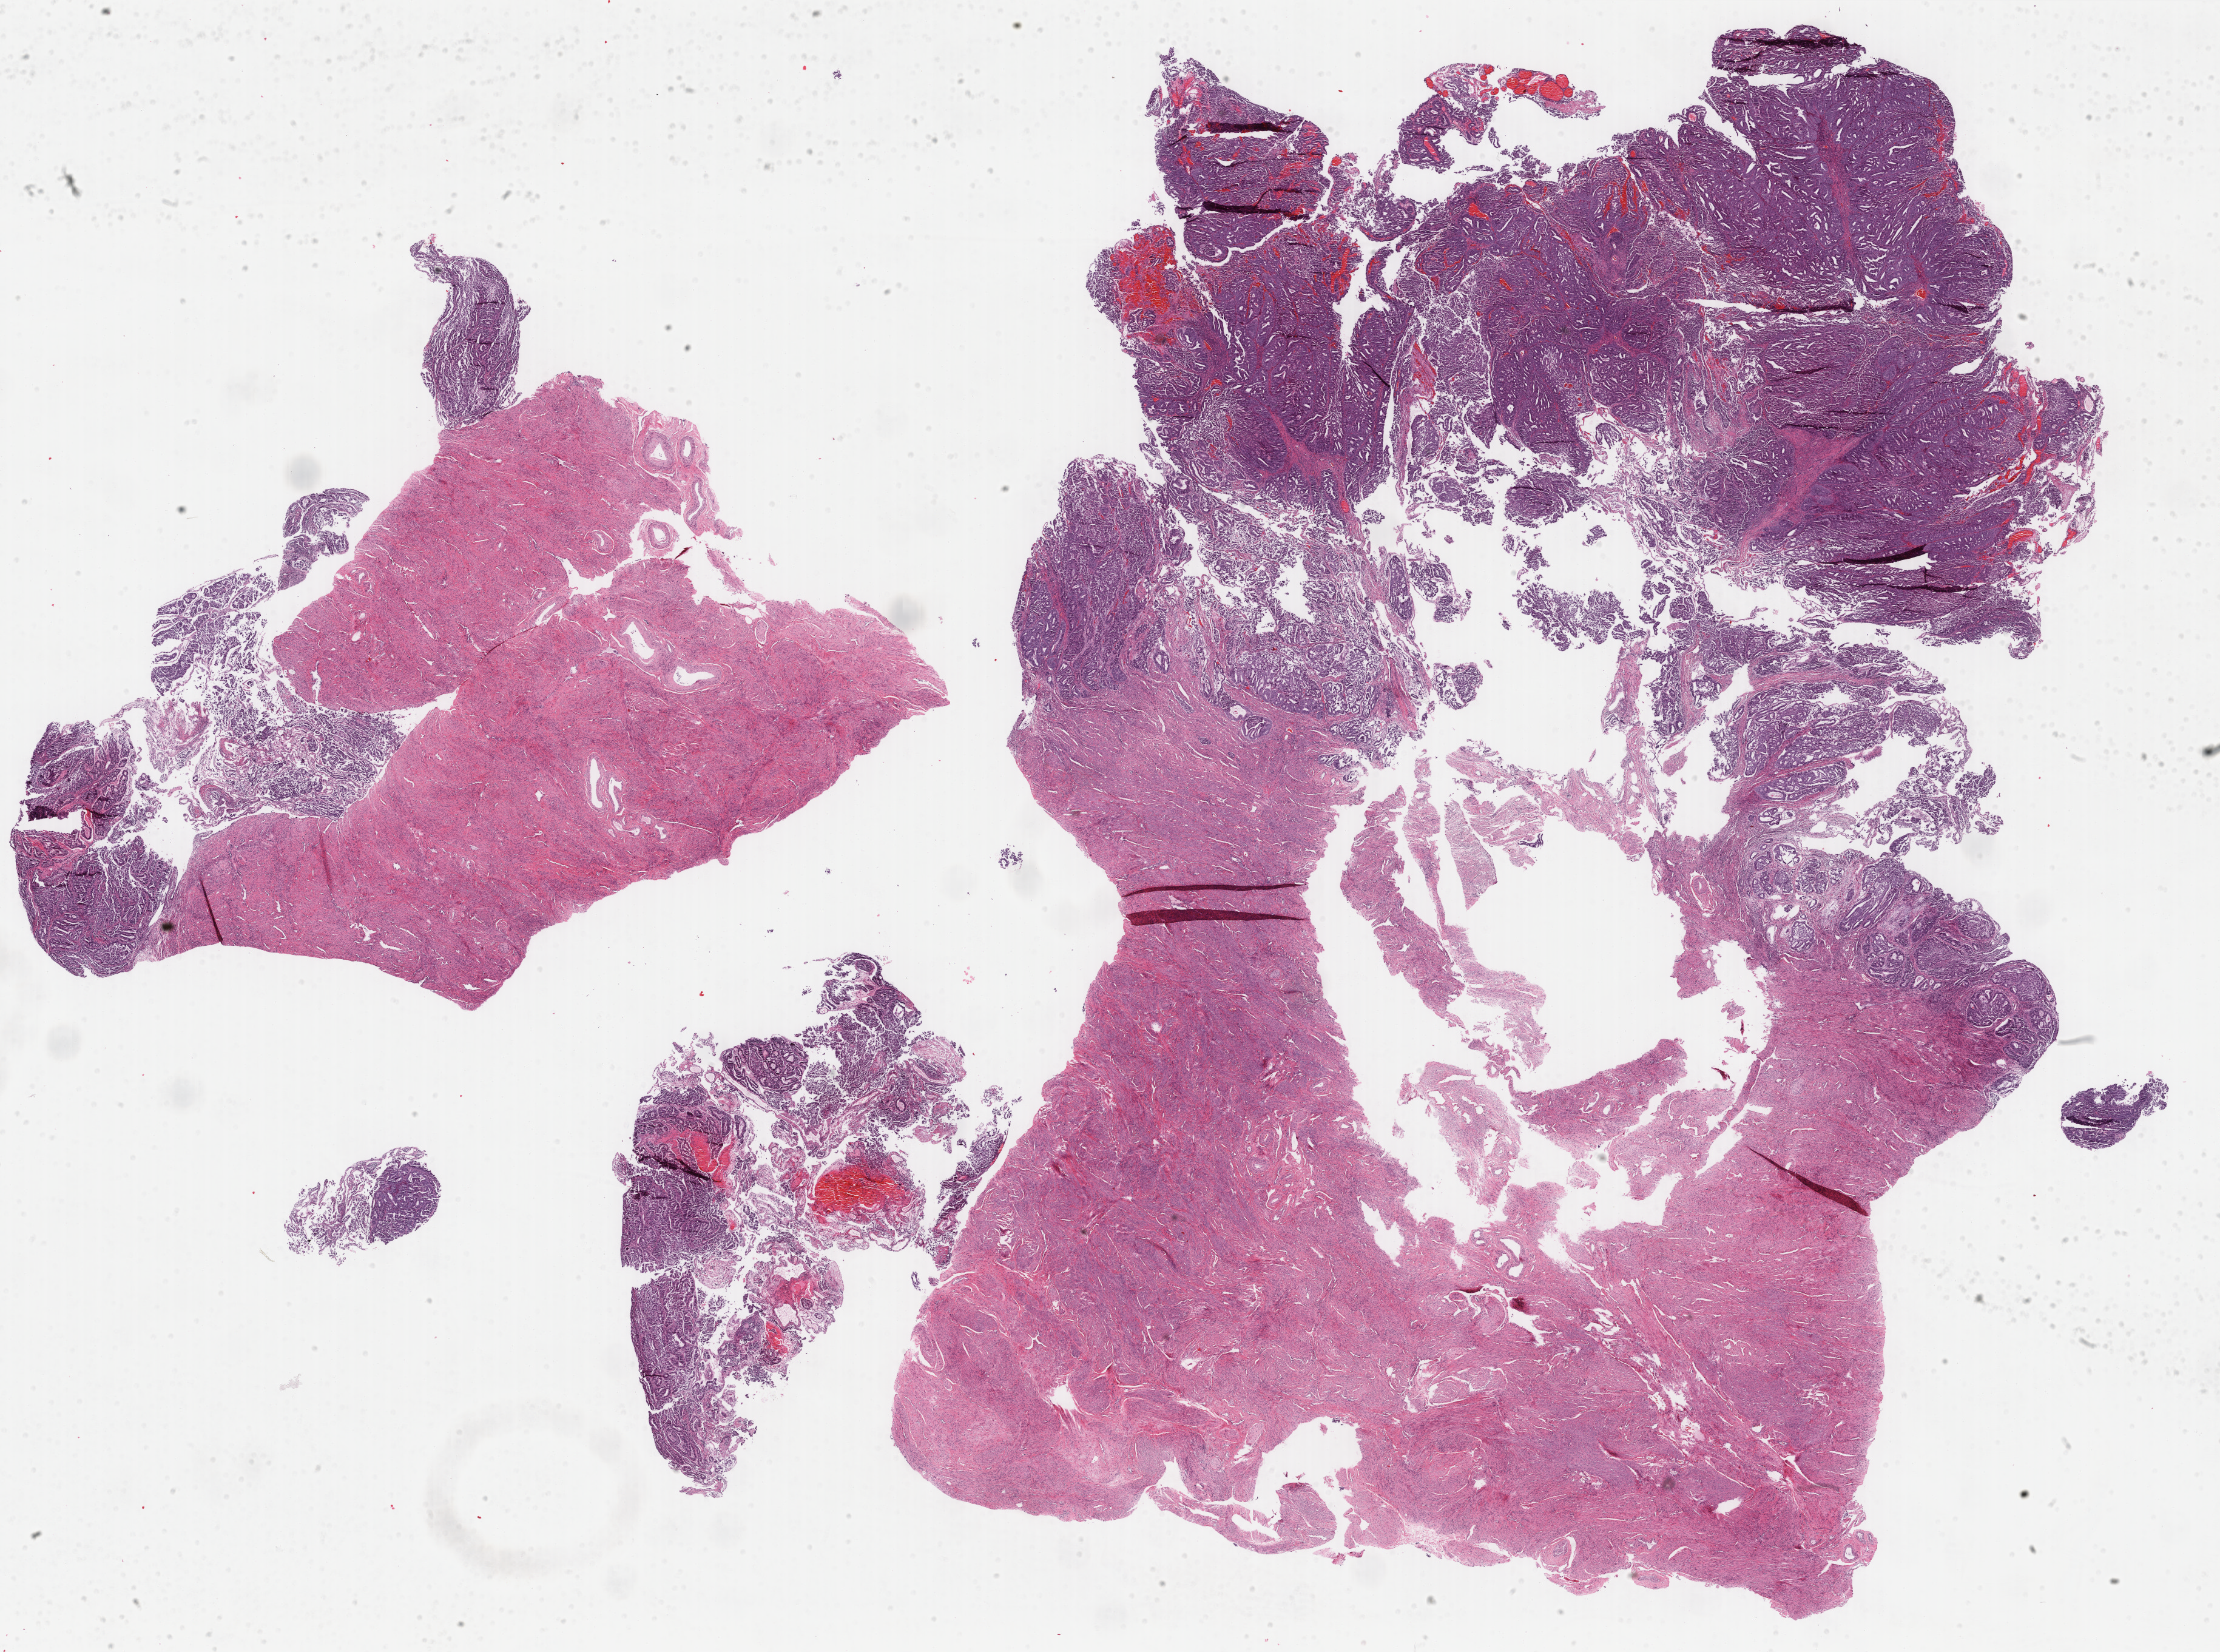
H&E-stained whole-slide image — whole scanned area (about 29.0 x 21.6 mm) shown as a low-resolution overview; formalin-fixed paraffin-embedded (FFPE) diagnostic section; sample: primary tumour, uterus. Female, age 64 years at initial diagnosis. Histologic grade: G1 (well differentiated).
Diagnosis: Endometrioid adenocarcinoma, NOS (endometrium). FIGO stage: IIIA.